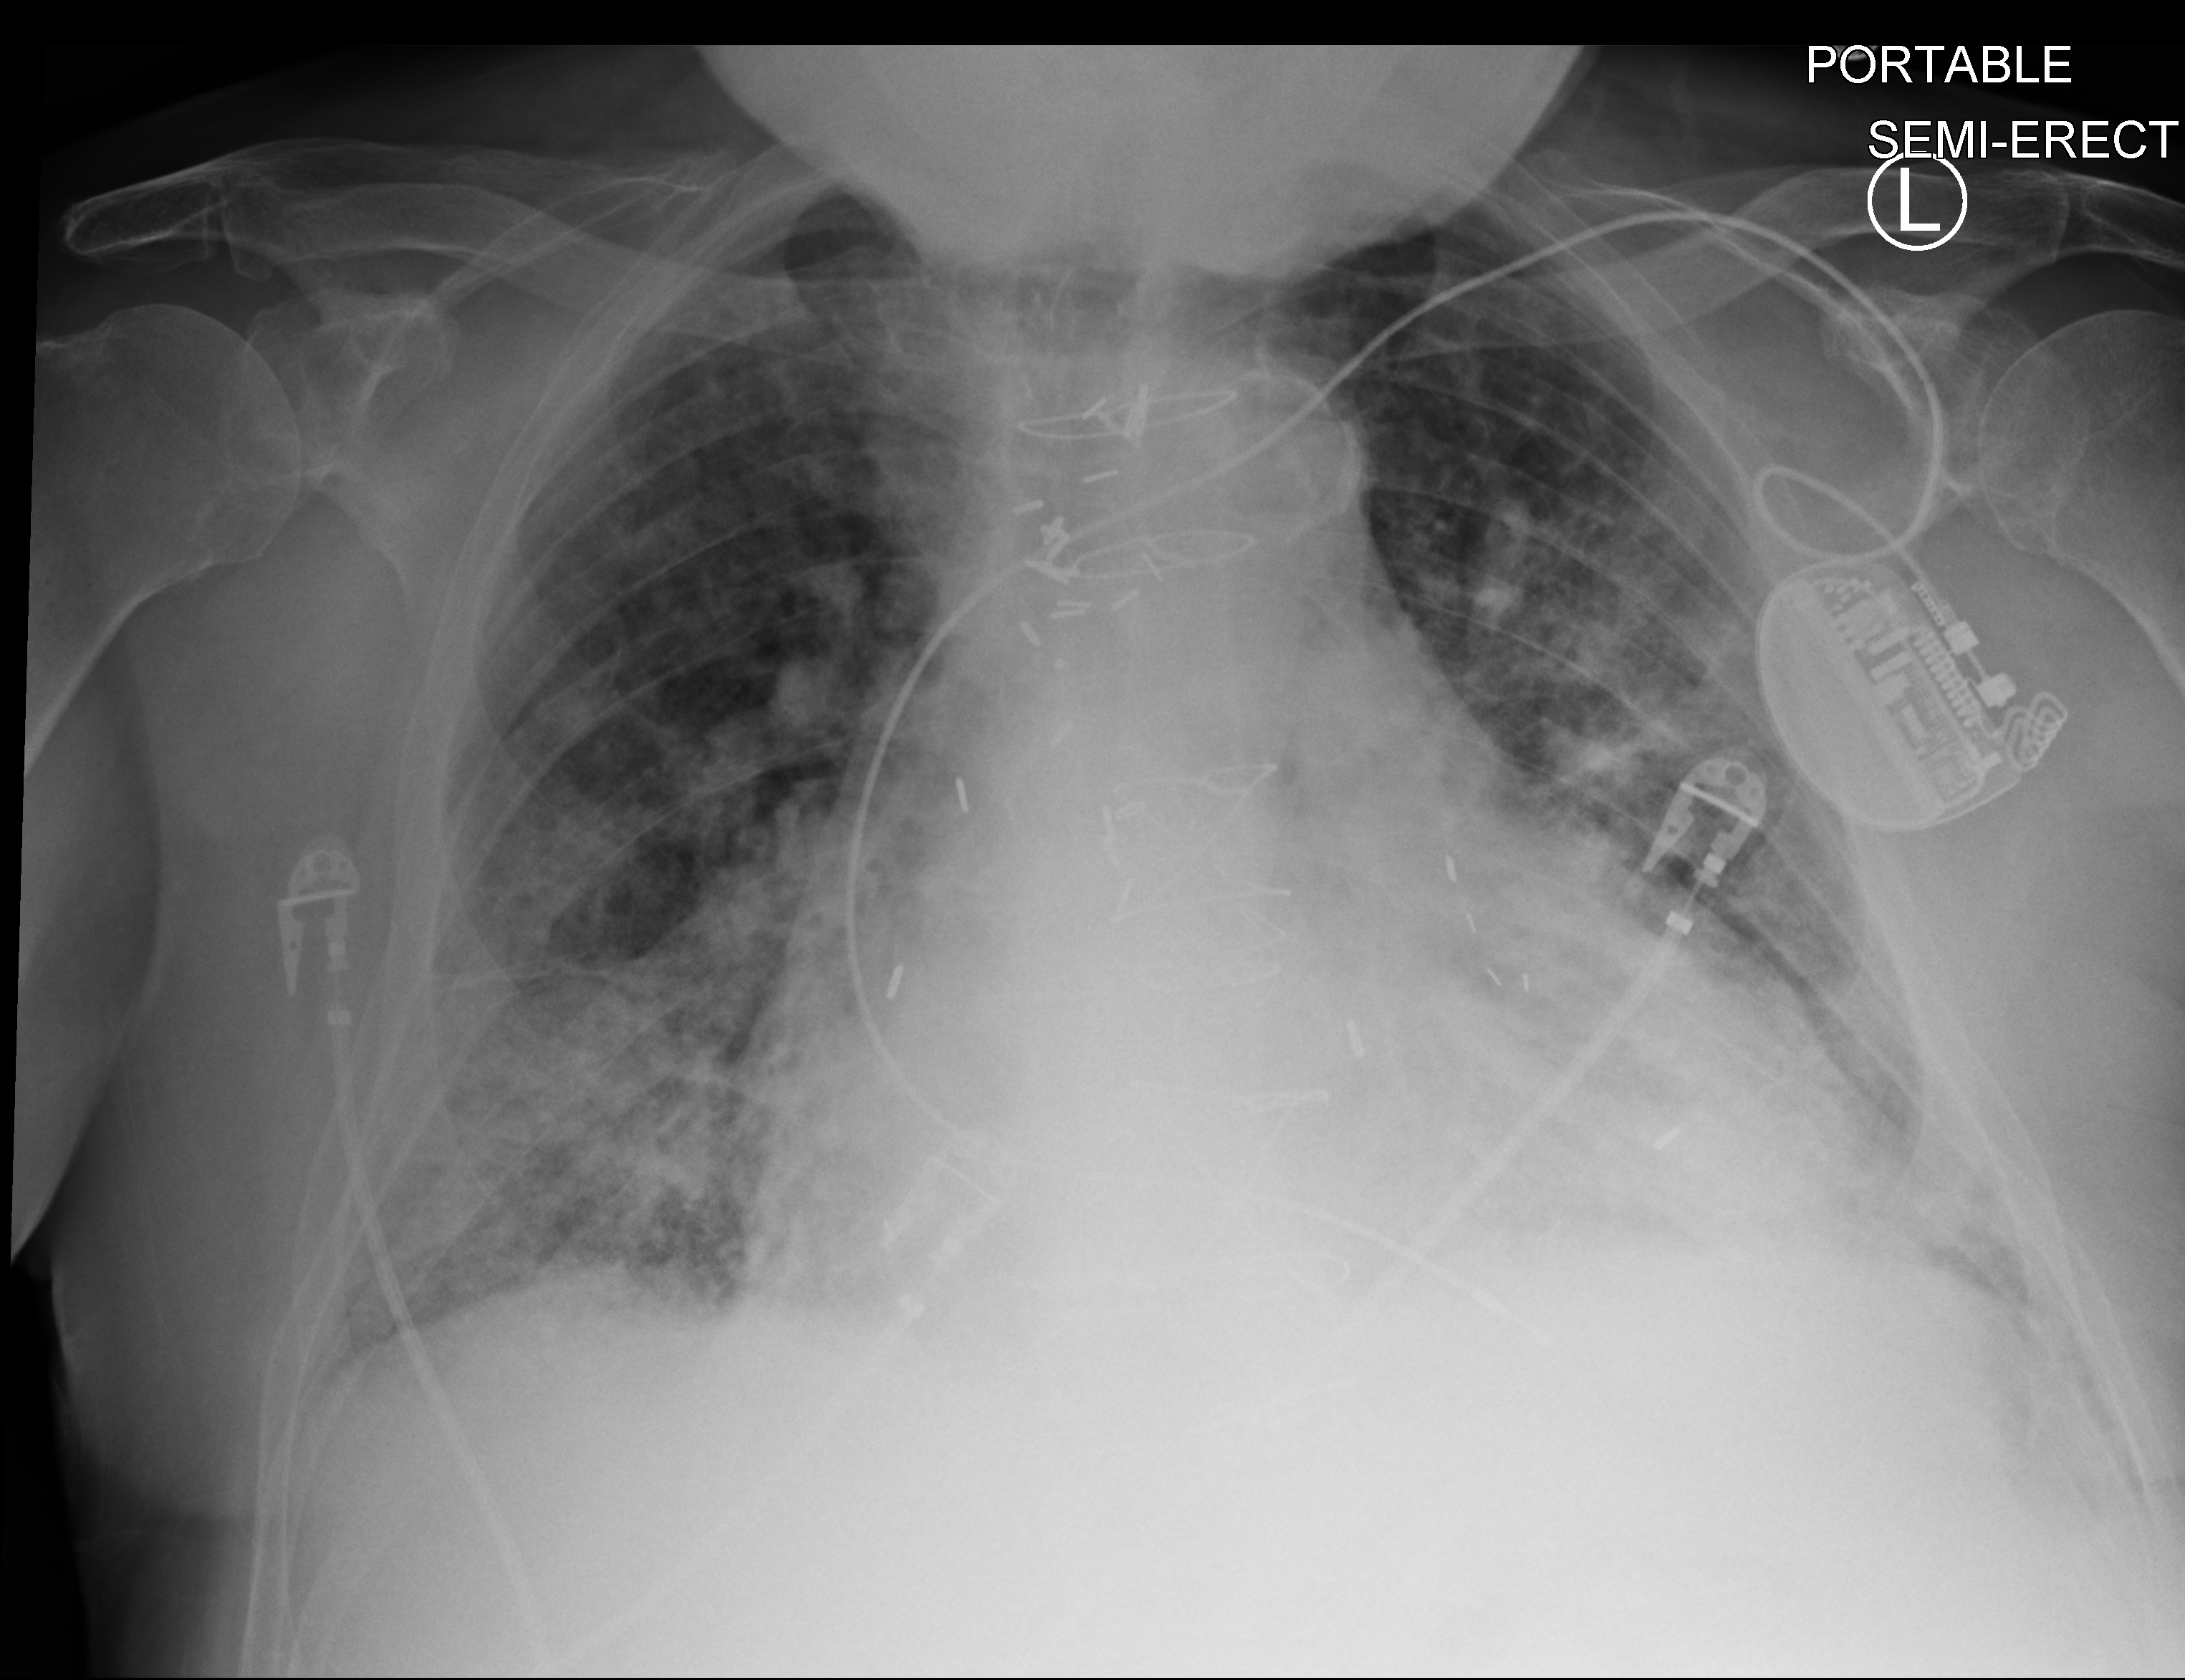
Bedside chest radiograph (computed radiography); anteroposterior (AP) projection. Patient hospitalised with COVID-19; male, aged 75–90 years.
From the hospital-stay record, not from the radiograph (when in the stay this image was taken is not recorded): mechanically ventilated during this hospital stay: yes.